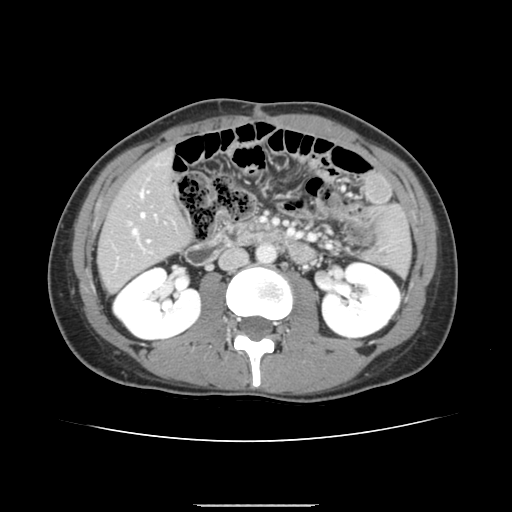
Contrast-enhanced abdominal CT, one axial slice. Position 59 of 150 along the scan axis. Intravenous contrast given. Soft-tissue window (W 400 / L 40 HU). 2.5 mm slice thickness. 512 × 512 image matrix. Female patient, age 32 years. From the clinical record (not read from this slice): diagnosis: colorectal cancer liver metastases, imaged before liver resection; multiple liver metastases: yes; largest metastasis: 0.7 cm.
Annotated regions visible in this slice (manually delineated by an expert):
- hepatic veins: bounding box (x1, y1, x2, y2) in pixels: (133, 191, 144, 234)
- liver: (99, 151, 189, 291)
- planned liver remnant (the part of the liver to remain after resection): (99, 152, 189, 290)
- portal vein (with intrahepatic branches): (129, 191, 150, 246)